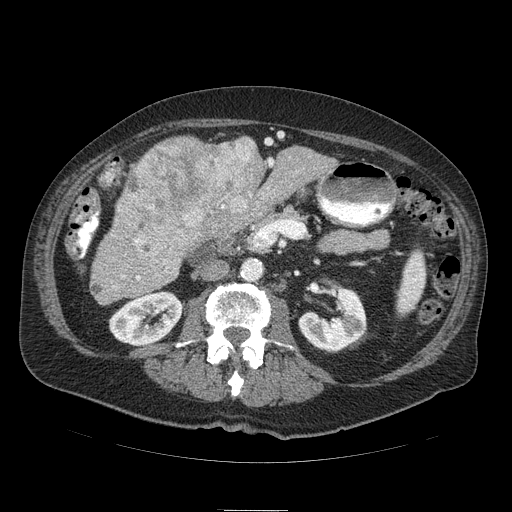
Contrast-enhanced abdominal CT (liver protocol), one axial slice. Position 30 of 103 along the scan axis. 120 kVp. Soft-tissue window (W 400 / L 40 HU). 512 × 512 image matrix, field of view 440 × 440 mm. From the clinical record (not read from this slice): diagnosis: hepatocellular carcinoma (patient treated with transarterial chemoembolisation; whether this scan precedes or follows treatment is not stated here); TNM stage (as recorded): Stage-IIIA; Child-Pugh class: B; tumour differentiation: well differentiated; tumour size: 13 cm.
Outlined on this slice (semi-automatically segmented with operator editing):
- liver parenchyma outside the tumour (the mass and vessels are separate outlines, so this box may not span the whole liver): bounding box <98,136,336,282> (left, top, right, bottom; pixels)
- mass: <119,137,265,261>
- liver vessels: <268,159,274,165>